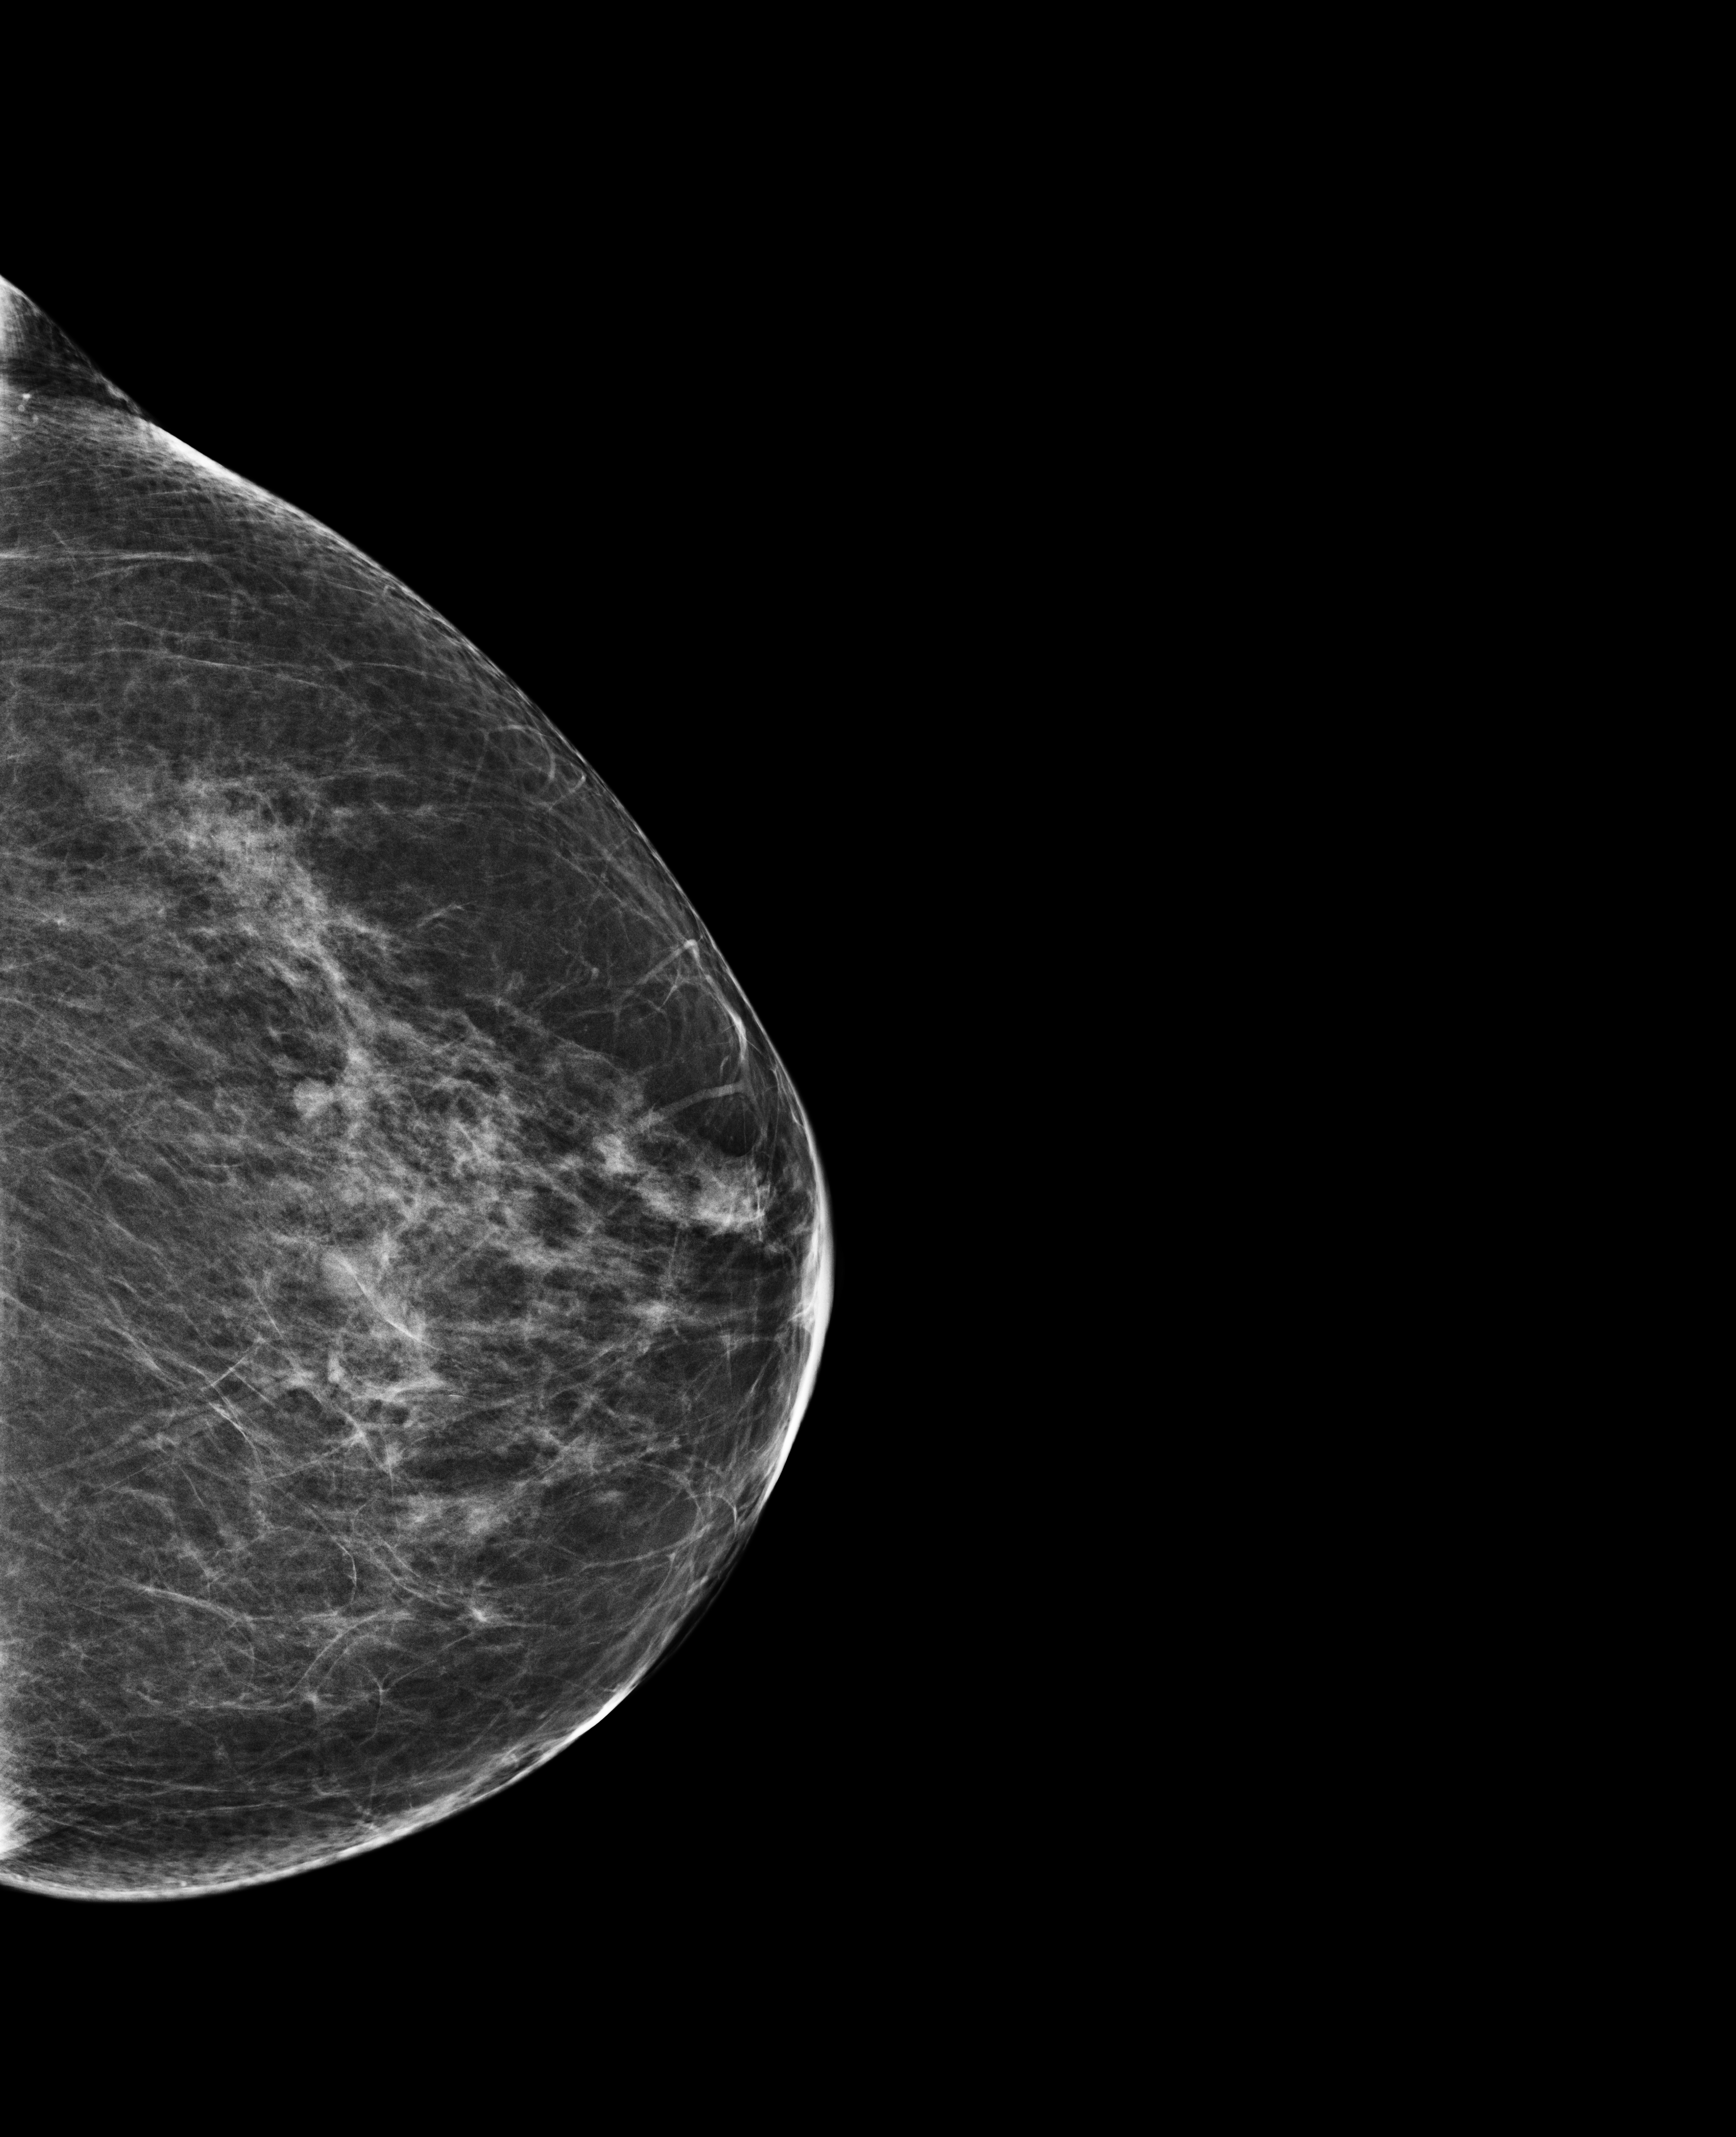
Annual screening mammography examination, compressed breast thickness 56 mm. Patient: female, 68 years.
Image type: full-field digital mammogram. Breast: left. Projection: CC view.